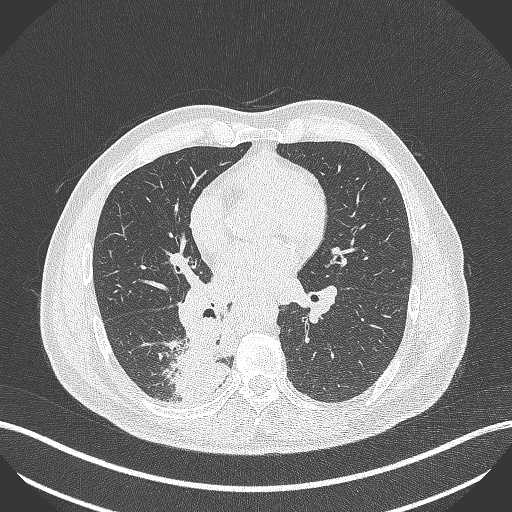
Chest CT, one axial slice; slice 228 of 451 in the series (ordered by position); 100 kVp; lung window (W 1500 / L -600 HU); 512 × 512 image matrix, field of view 400 × 400 mm. Male patient, age 61 years. From the clinical record (not read from this slice): clinical TNM (as recorded): T1 N0 M0.
Annotated regions visible in this slice (bounding box drawn by a radiologist):
- lung tumour (recorded histology: small cell carcinoma): bounding box <159,315,228,398> (left, top, right, bottom; pixels)